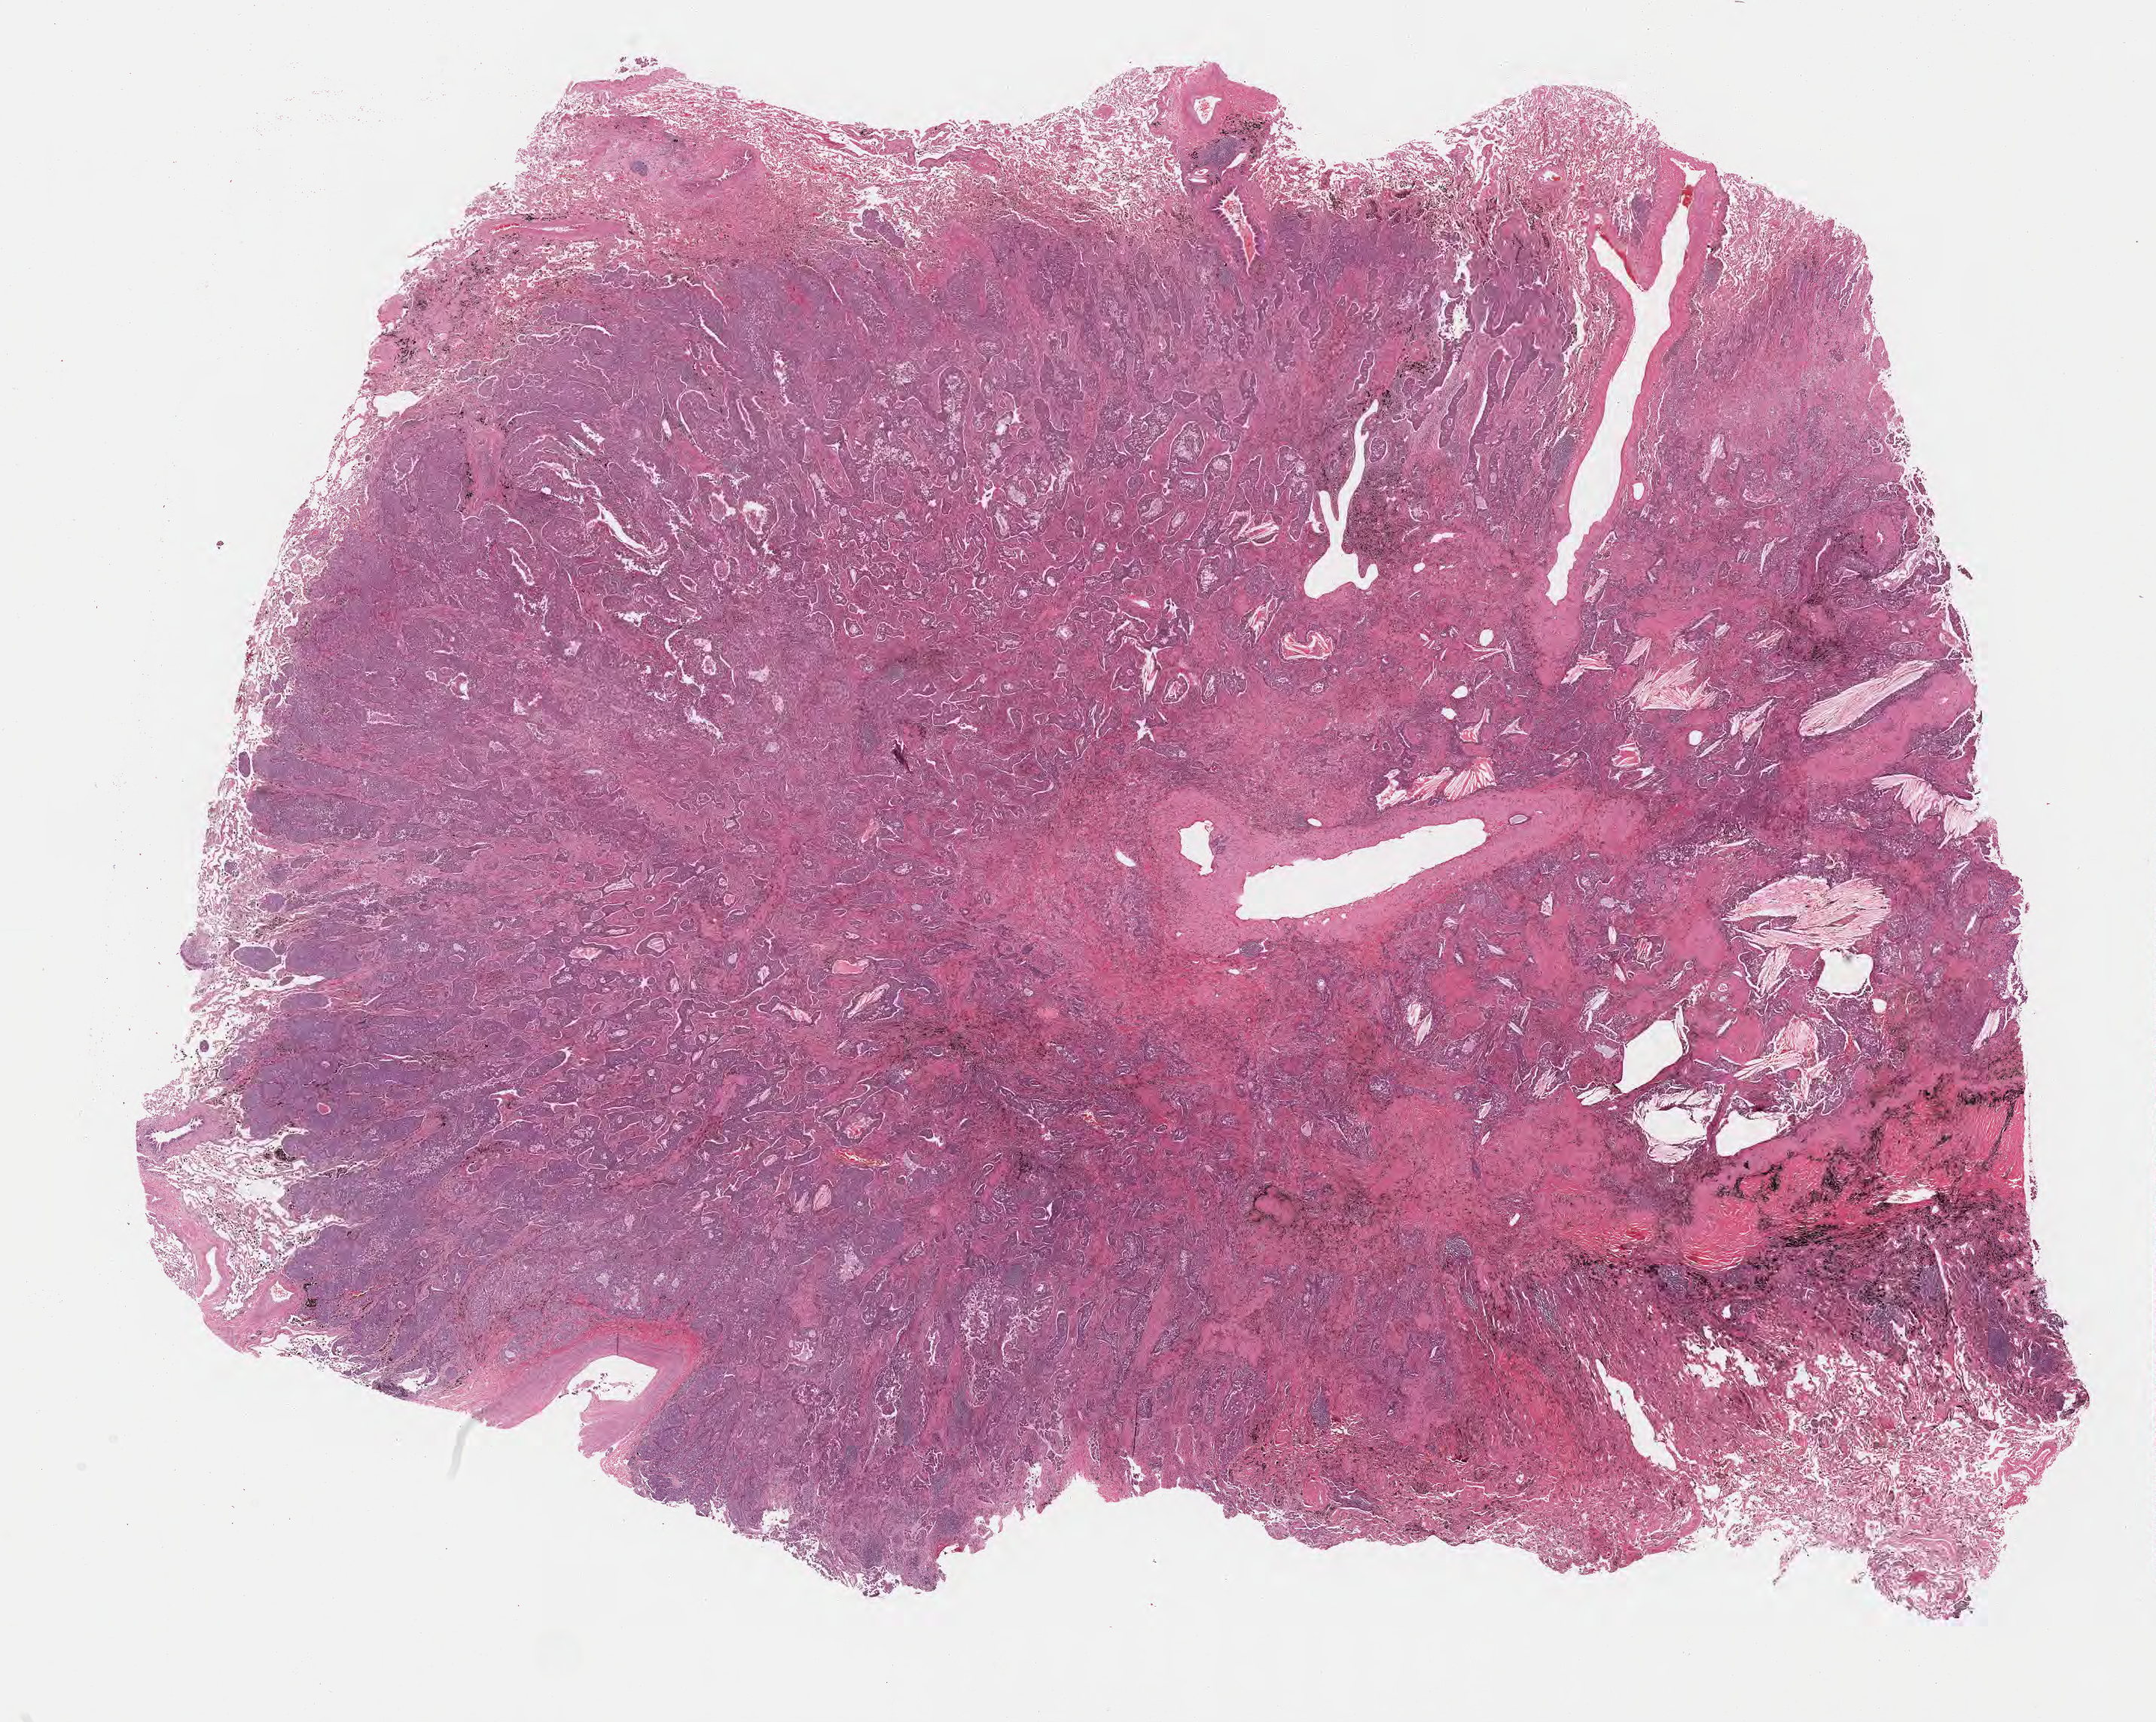
Whole-slide image, H&E stain, whole scanned area (about 23.2 x 18.5 mm) shown as a low-resolution overview; formalin-fixed paraffin-embedded section; primary tumor; anatomic site: upper lobe of right lung. Patient: male, age 69 years.
Diagnosis: Adenocarcinoma, NOS.